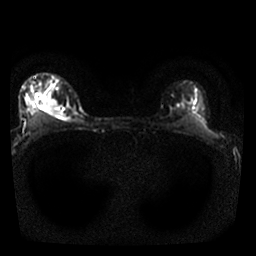
Breast MRI, one axial slice. Slice 23 of 25 in the series (ordered by position). Diffusion-weighted series; image 2 of 4 stored at this slice position (different b-values; order by instance number). 1.5 T. 4 mm slice thickness. 256 × 256 image matrix. Female patient.
Annotated regions visible in this slice (outlined manually by an expert reader):
- tumour on diffusion-weighted imaging: bounding box [x1, y1, x2, y2] px = [40, 99, 59, 116]